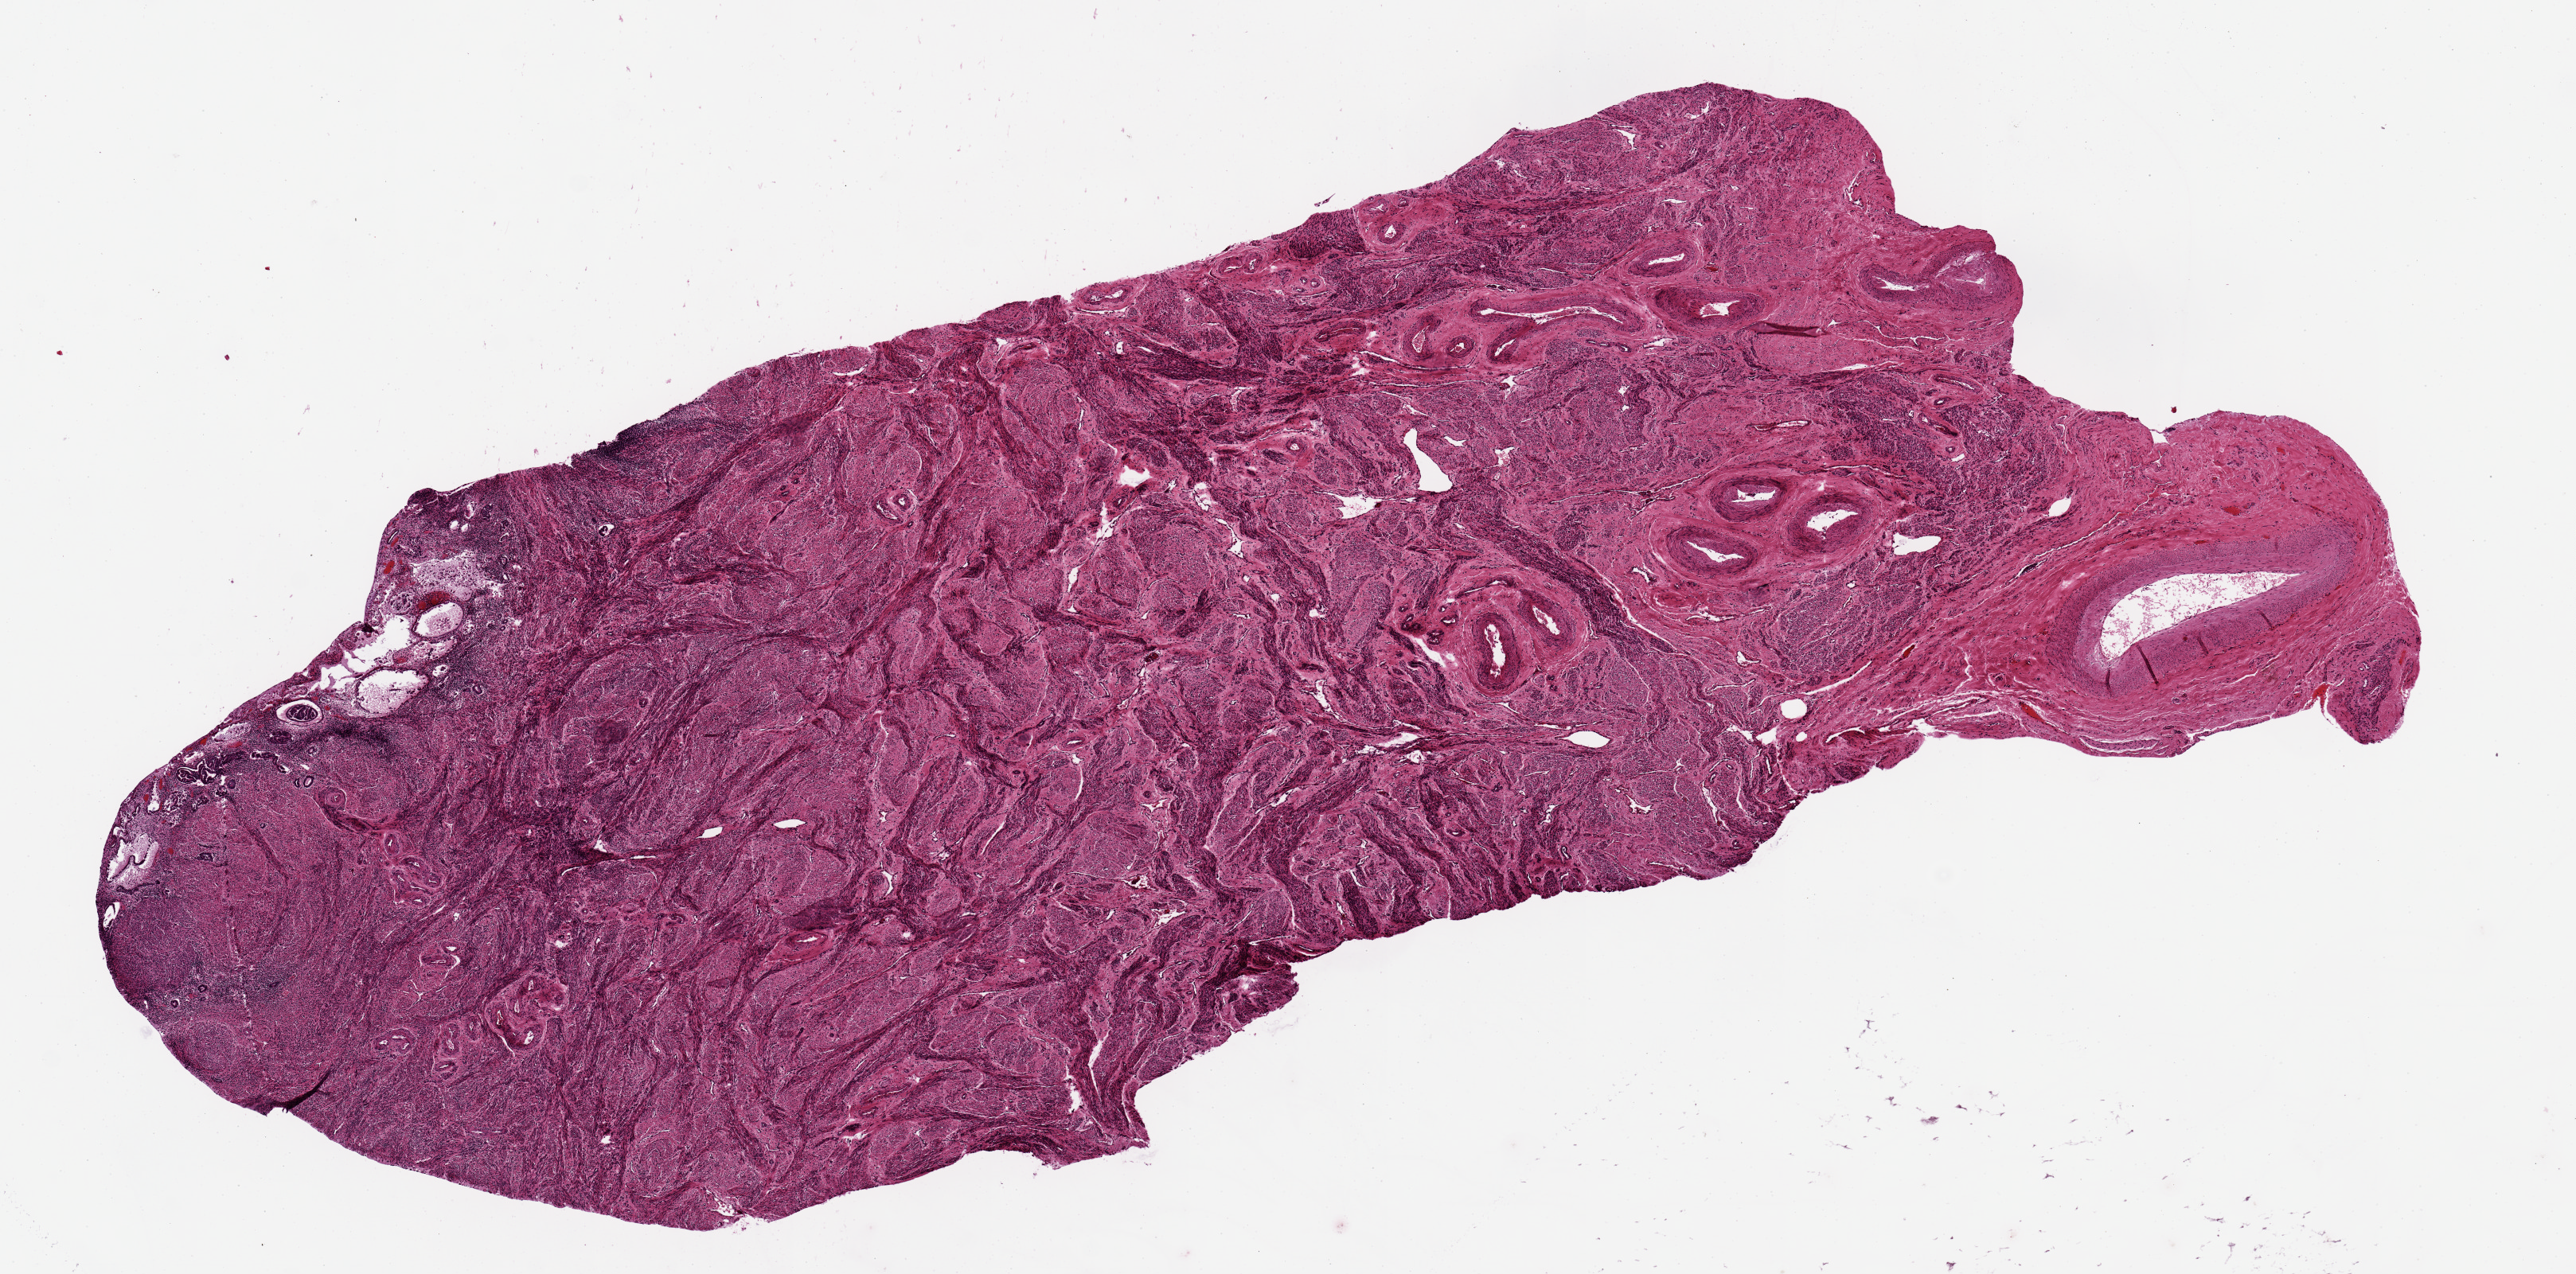
Whole-slide image, hematoxylin and eosin (H&E) stain — whole scanned area (about 12.8 x 6.3 mm) shown as a low-resolution overview; PAXgene-fixed, paraffin-embedded tissue; section of uterus (target tissue); donor tissue sample. Female donor.
Review note (as recorded): (glands/stroma); 1 (myometrium. A 0.8 x 2.8mm glandular focus on one pole of a 10x 4mm aliquot.